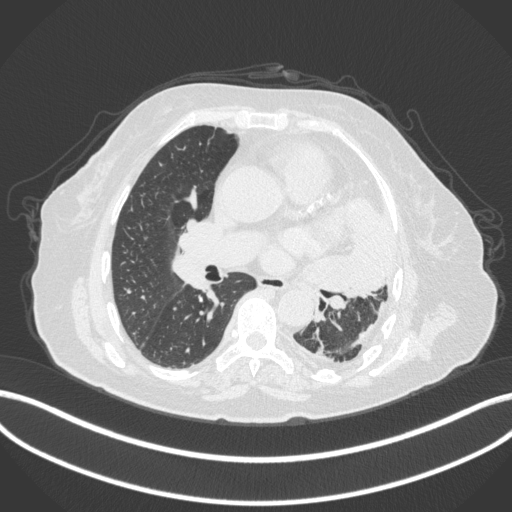
Chest CT, one axial slice. Position 194 of 399 along the scan axis. Reconstruction kernel B31f. 120 kVp. Lung window (W 1500 / L -600 HU). 1 mm slice thickness. 512 × 512 image matrix, field of view 400 × 400 mm. Patient: female, 75 years. From the clinical record (not read from this slice): clinical TNM (as recorded): T3 N3 M1.
Outlined on this slice (bounding box drawn by a radiologist):
- lung tumour (recorded histology: adenocarcinoma): box from (x=294, y=199) to (x=403, y=302) px